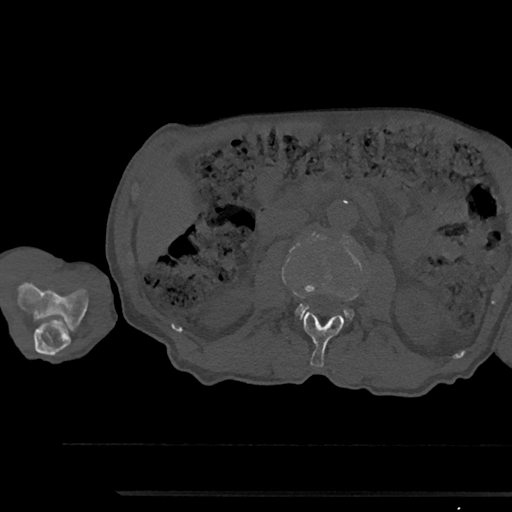
CT including the spine, one axial slice; slice 533 of 797 in the series (ordered by position); reconstruction kernel Br40s/3; 120 kVp; bone window (W 1800 / L 400 HU); 0.5 mm slice thickness; 512 × 512 image matrix, field of view 367 × 367 mm. Male patient, age 79 years. Case-level facts recorded for this patient, not image findings: primary cancer: prostate.
Outlined on this slice (semi-automatic segmentation, software-assisted and operator-edited):
- L2 vertebra: bounding box <302,312,344,367> (left, top, right, bottom; pixels)
- L3 vertebra: <296,285,354,319>